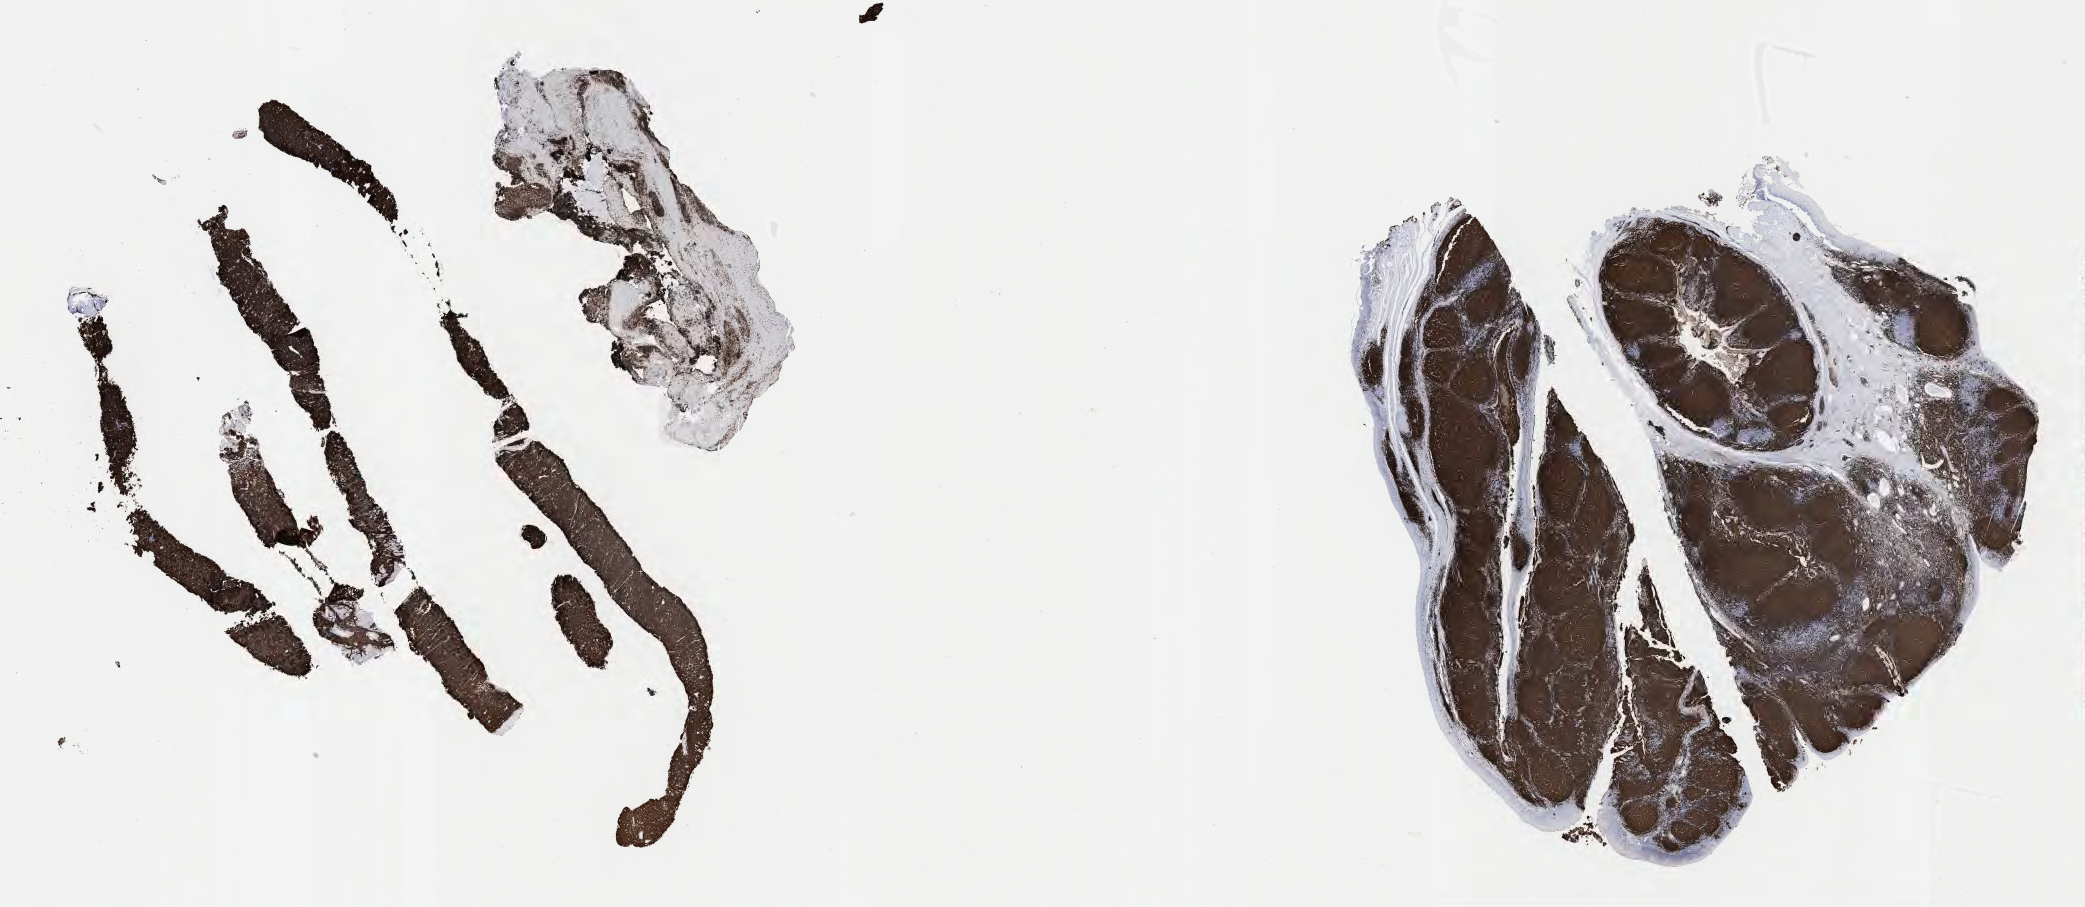
Whole-slide image, immunohistochemical stain for CD20, shown as a low-resolution overview of the whole scanned area (about 33.7 x 14.7 mm). Specimen: tumor tissue. Patient: male, 29 years old.
- diagnosis: Burkitt lymphoma, NOS